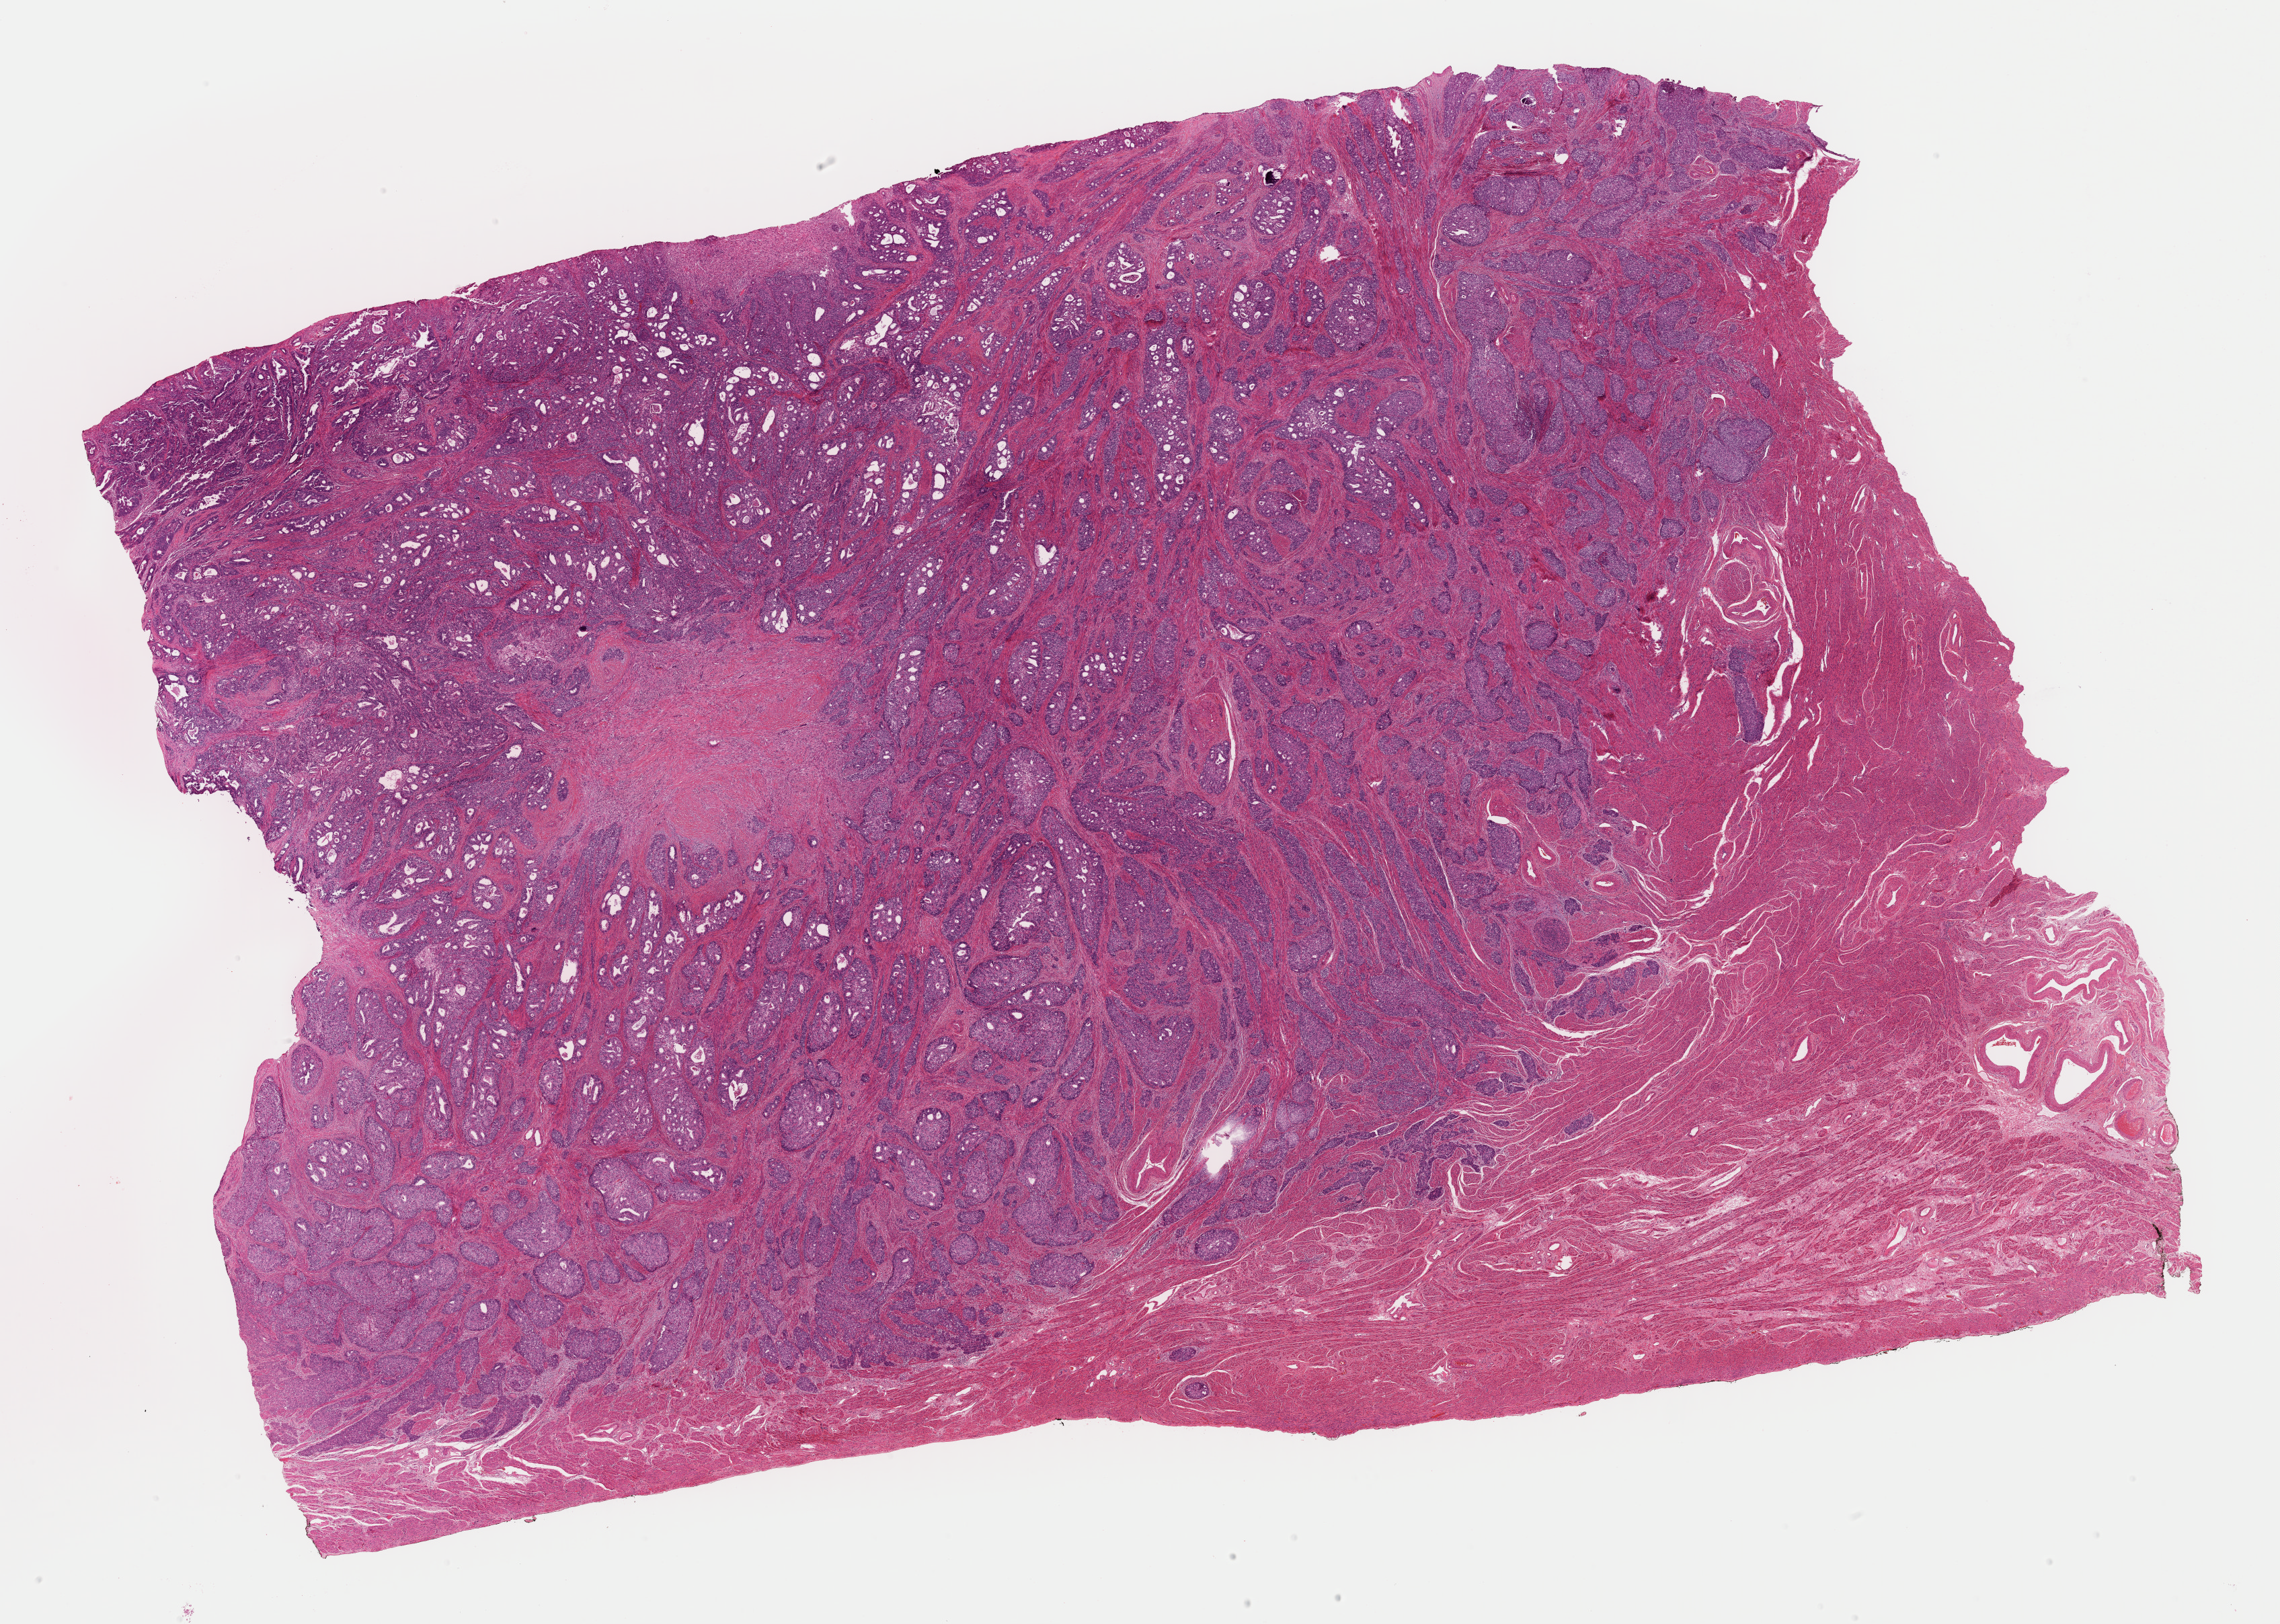
Digitized H&E tissue section (whole slide), shown as a low-resolution overview of the whole scanned area (about 26.8 x 19.1 mm). Formalin-fixed paraffin-embedded (FFPE) diagnostic section. Uterus, primary tumour sample. Female, age 63 years at initial diagnosis. Histologic grade: G3 (poorly differentiated).
FIGO stage: IIIA. Diagnosis: Endometrioid adenocarcinoma, NOS.